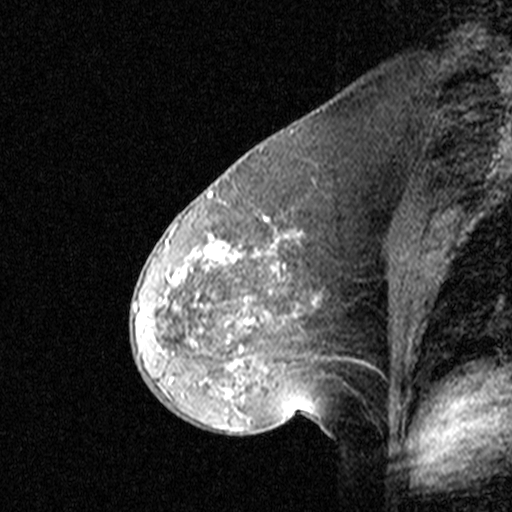
Breast MRI (dynamic contrast-enhanced), one sagittal slice; slice 20 of 44 in the series (ordered by position); dynamic contrast-enhanced study with each time point stored as its own series, time point 2 of 3 at this slice position (early post-contrast, ordered by acquisition time); 1.5 T; TE 4.5 ms, TR 11 ms; 3 mm slice thickness; 512 × 512 image matrix, field of view 200 × 200 mm. Patient: female, 46 years. Case-level facts recorded for this patient, not image findings: setting: breast cancer imaged before/during neoadjuvant chemotherapy; receptor status: HER2-positive.
Annotated regions visible in this slice (semi-automatic segmentation, software-assisted and operator-edited):
- analysis volume of interest (the breast-tissue region the enhancement analysis was run in; not a lesion): bounding box (x1, y1, x2, y2) in pixels: (144, 172, 359, 393)
- tumour enhancement mask (voxels above the 90 % enhancement threshold inside the analysis volume of interest): (146, 194, 339, 380)